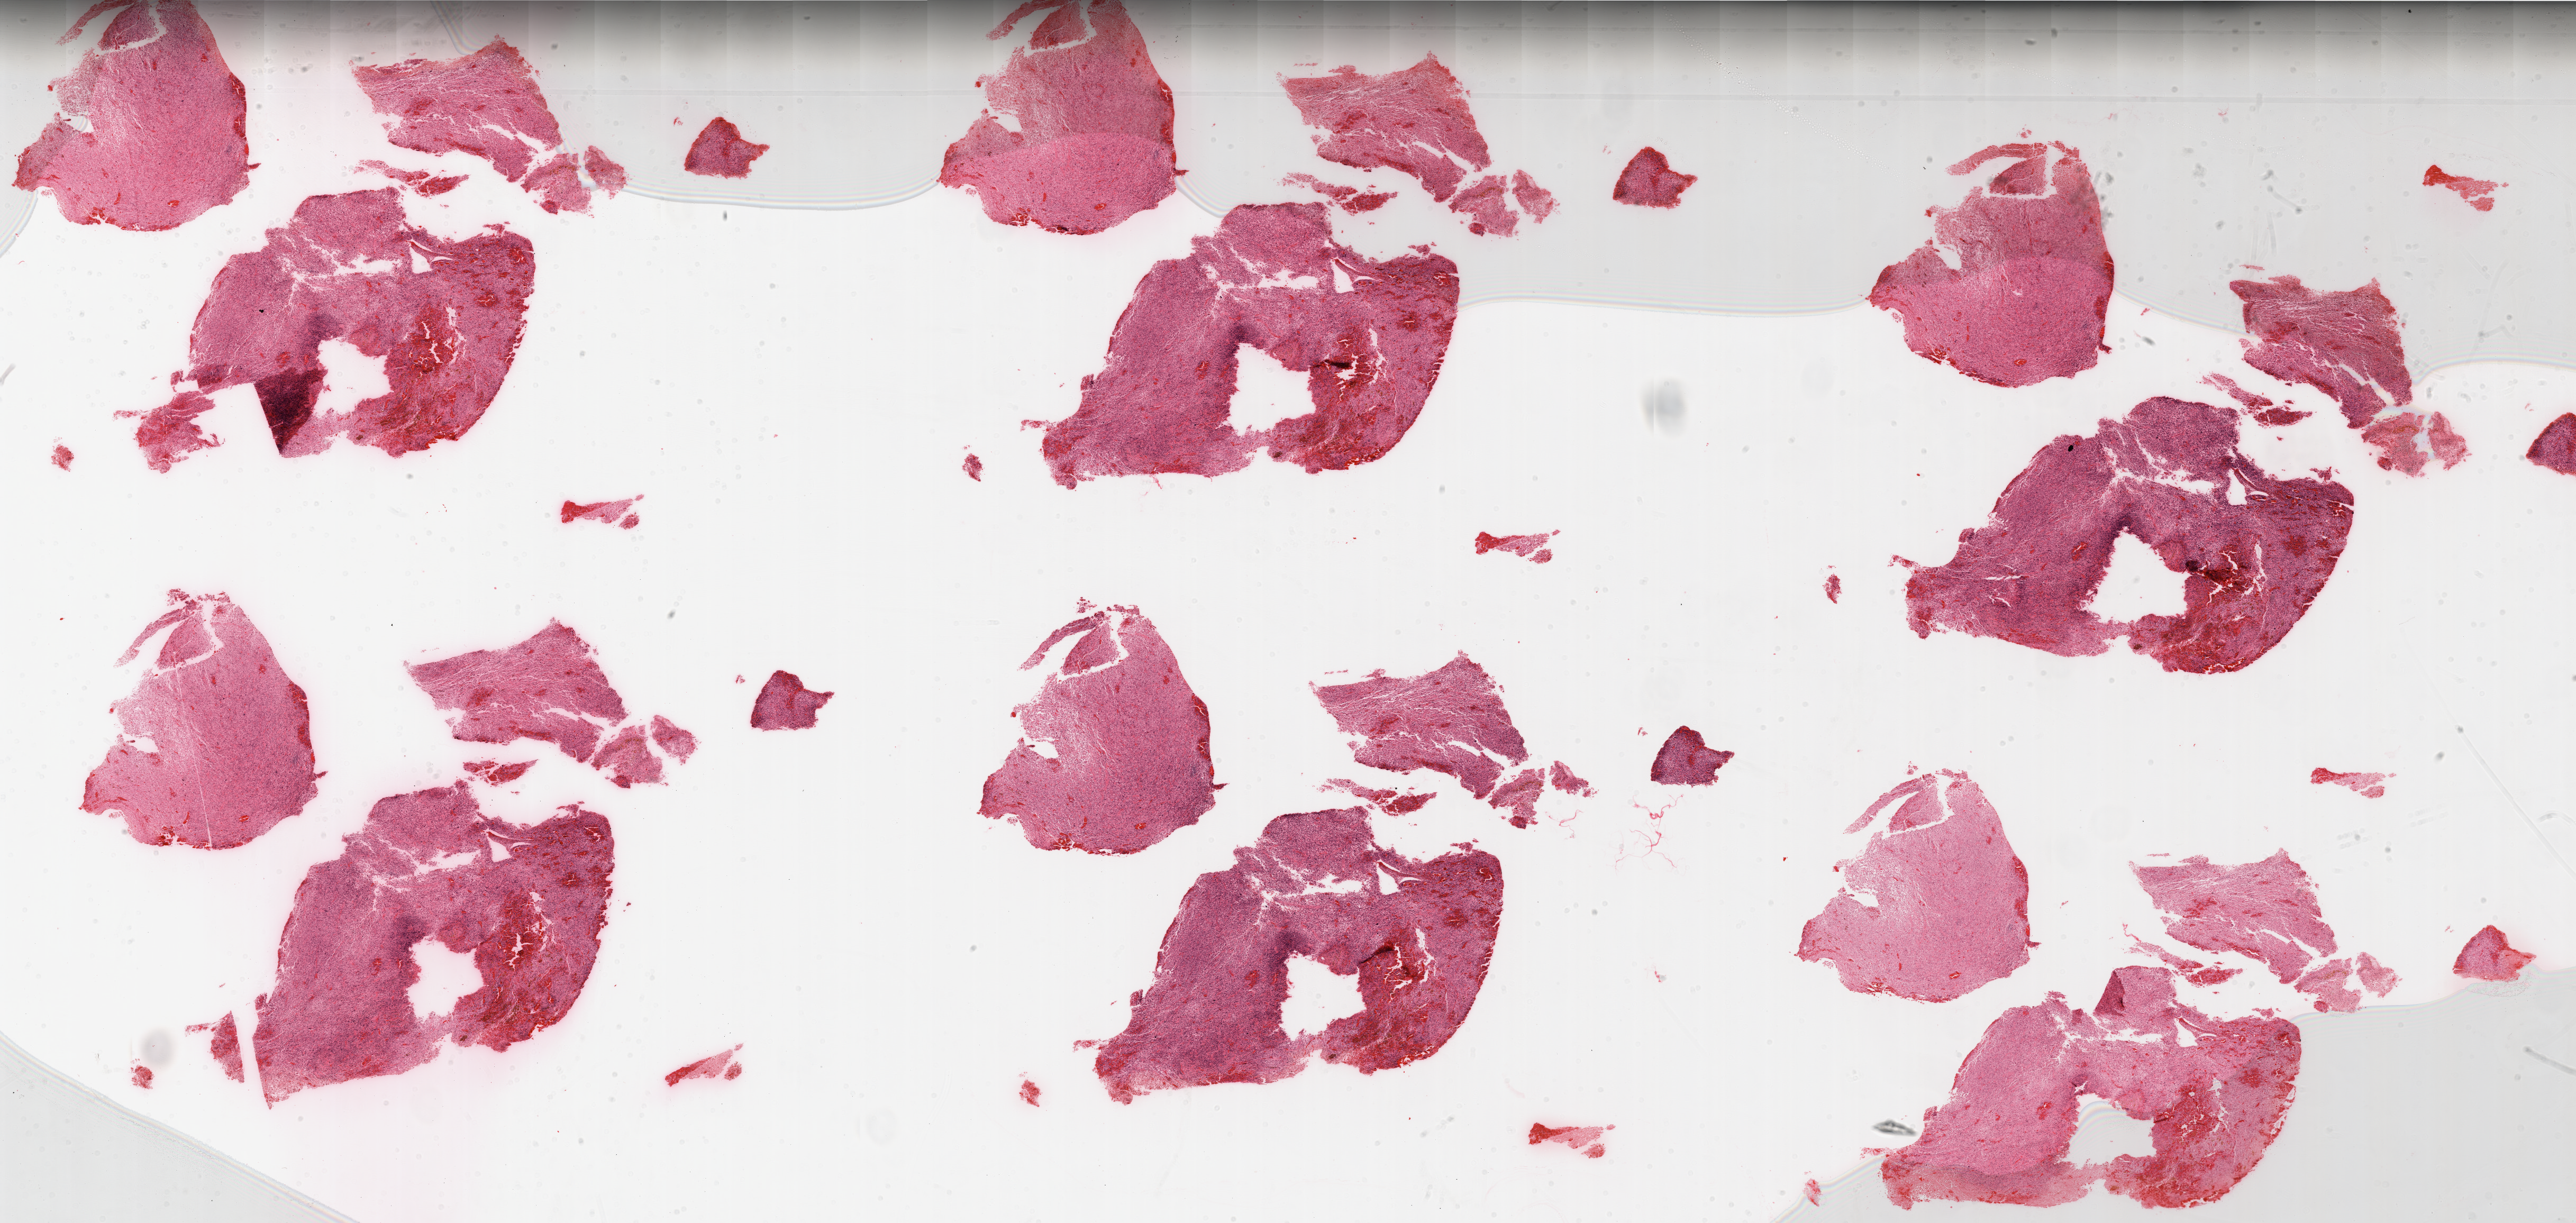
H&E whole-slide image — low-resolution overview of the scanned area, about 39.0 x 18.5 mm (from a 20x scan), formalin-fixed paraffin-embedded (FFPE) diagnostic section, sample: primary tumour, brain. Male patient; age at initial diagnosis 63 years.
Histologic diagnosis: Glioblastoma.